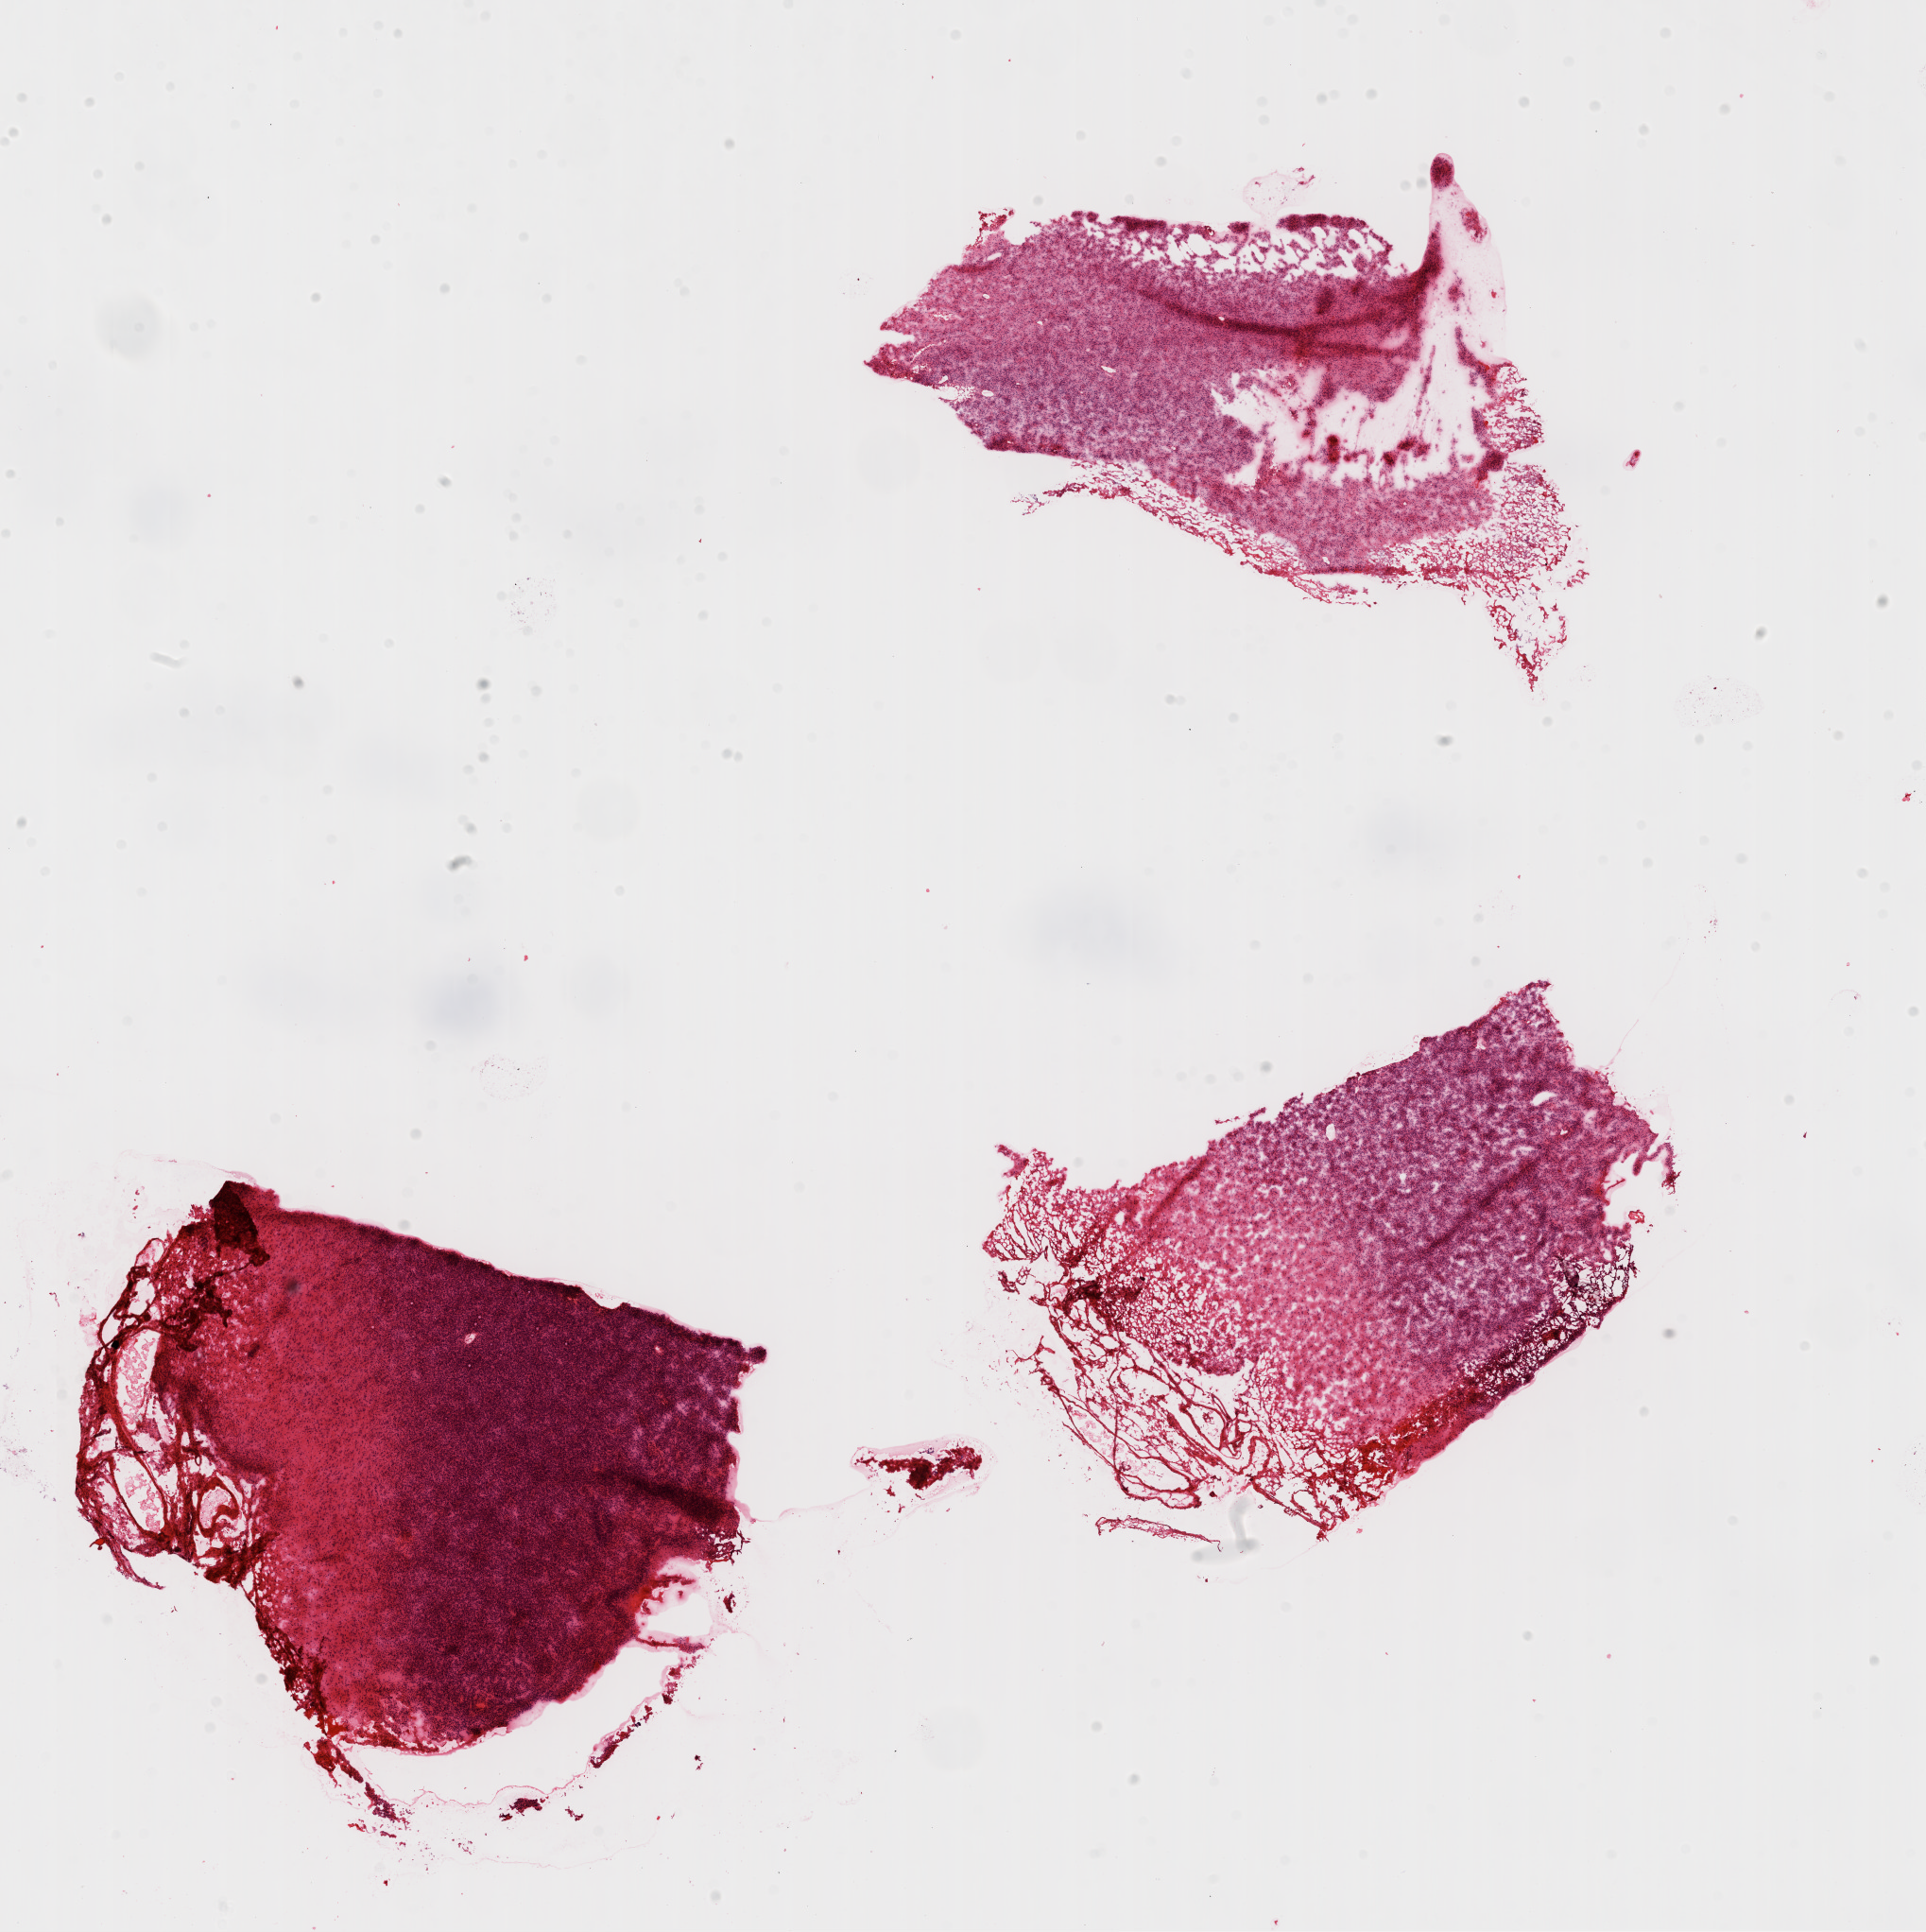
Digitized H&E-stained tissue section (whole slide), shown as a low-resolution overview of the whole scanned area (about 16.4 x 16.5 mm, acquisition: 20x scan), frozen section from the bottom of the tissue portion, primary tumour sample from the brain. Male, age 62 years at initial diagnosis. Pathologist review of this section (percent, as recorded): tumour cells 70%, tumour nuclei 90%.
Histologic diagnosis: Glioblastoma.